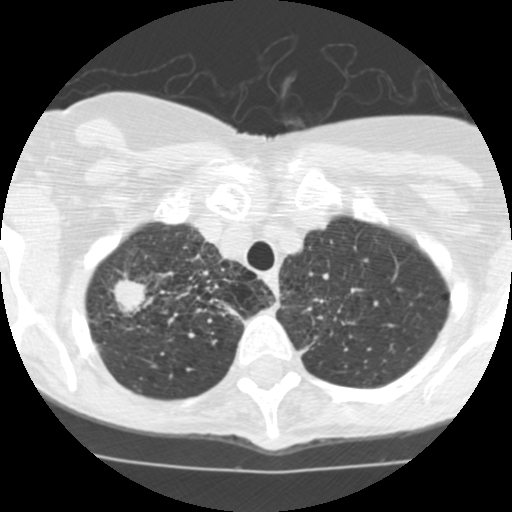
Chest CT (low-dose screening protocol), one axial image, second annual screen, lung window (W 1500 / L -600 HU), 2.5 mm slice thickness, slice 19 of 115 in the series. Female participant, aged 68 years at enrolment. Current smoker at enrolment.
• Expert-annotated lung lesion, bounding box [x1, y1, x2, y2] px = [90, 265, 157, 336].
• The screening reader recorded 3 non-calcified nodules or masses ≥4 mm on this exam (right upper lobe, right upper lobe, right middle lobe); which of them this box marks is not recorded.
• Official screen result: positive, other.
• Participant outcome: lung cancer diagnosed 36 days after this screen — large cell neuroendocrine carcinoma, right upper lobe, undifferentiated (G4), stage IB (AJCC 6th edition), 22 mm at pathology.